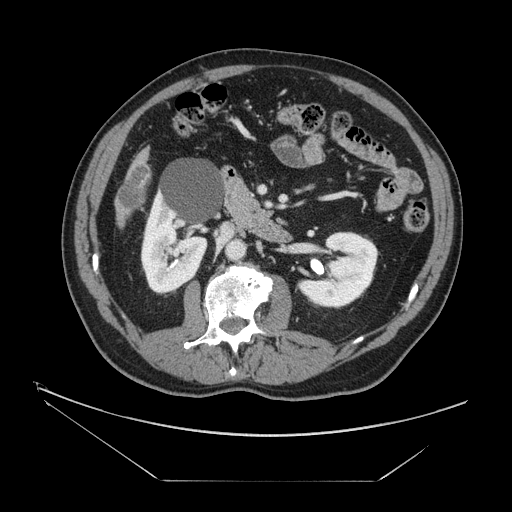
Contrast-enhanced abdominal CT, one axial slice. Position 51 of 161 along the scan axis. Intravenous contrast given. Soft-tissue window (W 400 / L 40 HU). 512 × 512 image matrix. Male patient, age 65 years. From the clinical record (not read from this slice): diagnosis: colorectal cancer liver metastases, imaged before liver resection; multiple liver metastases: yes; largest metastasis: 4.2 cm; disease in both lobes: yes.
Annotated regions visible in this slice (manually delineated by an expert):
- liver: bounding box (x1, y1, x2, y2) in pixels: (118, 154, 149, 222)
- liver metastasis: (121, 168, 149, 207)